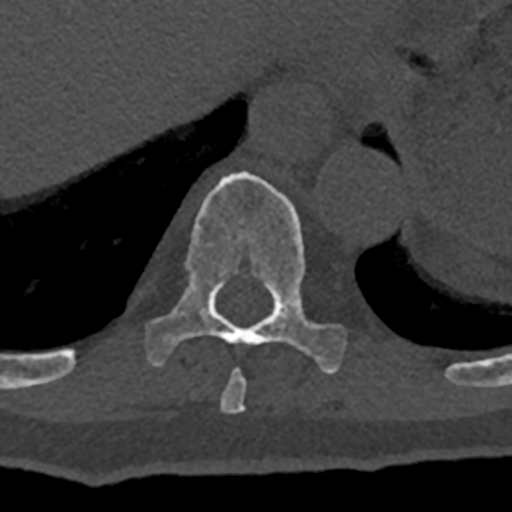
CT including the spine, one axial slice. Slice 606 of 797 in the series (ordered by position). Bone window (W 1800 / L 400 HU). 512 × 512 image matrix, field of view 160 × 160 mm. Patient: male, 74 years. From the clinical record (not read from this slice): primary cancer: renal.
Structures marked on this image (semi-automatic segmentation, software-assisted and operator-edited):
- T10 vertebra: bounding box <70,171,345,374> (left, top, right, bottom; pixels)
- T9 vertebra: <220,369,246,413>